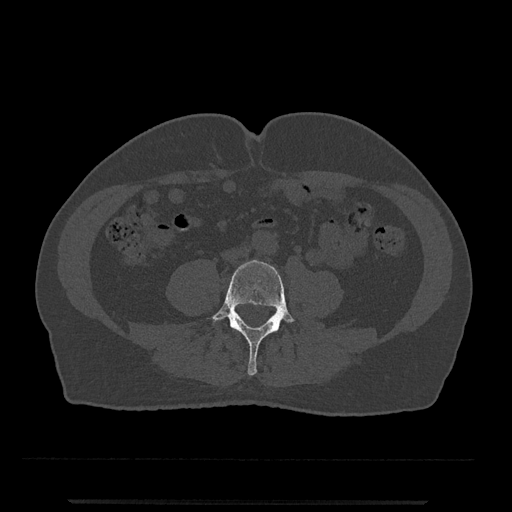
CT including the spine, one axial slice. Position 137 of 797 along the scan axis. Reconstruction kernel Br40s/3. 120 kVp. Bone window (W 1800 / L 400 HU). 0.5 mm slice thickness. 512 × 512 image matrix. Patient: male, 63 years. From the clinical record (not read from this slice): primary cancer: prostate.
Annotated regions visible in this slice (semi-automatically segmented with operator editing):
- L4 vertebra: bounding box [x1, y1, x2, y2] px = [207, 260, 295, 376]